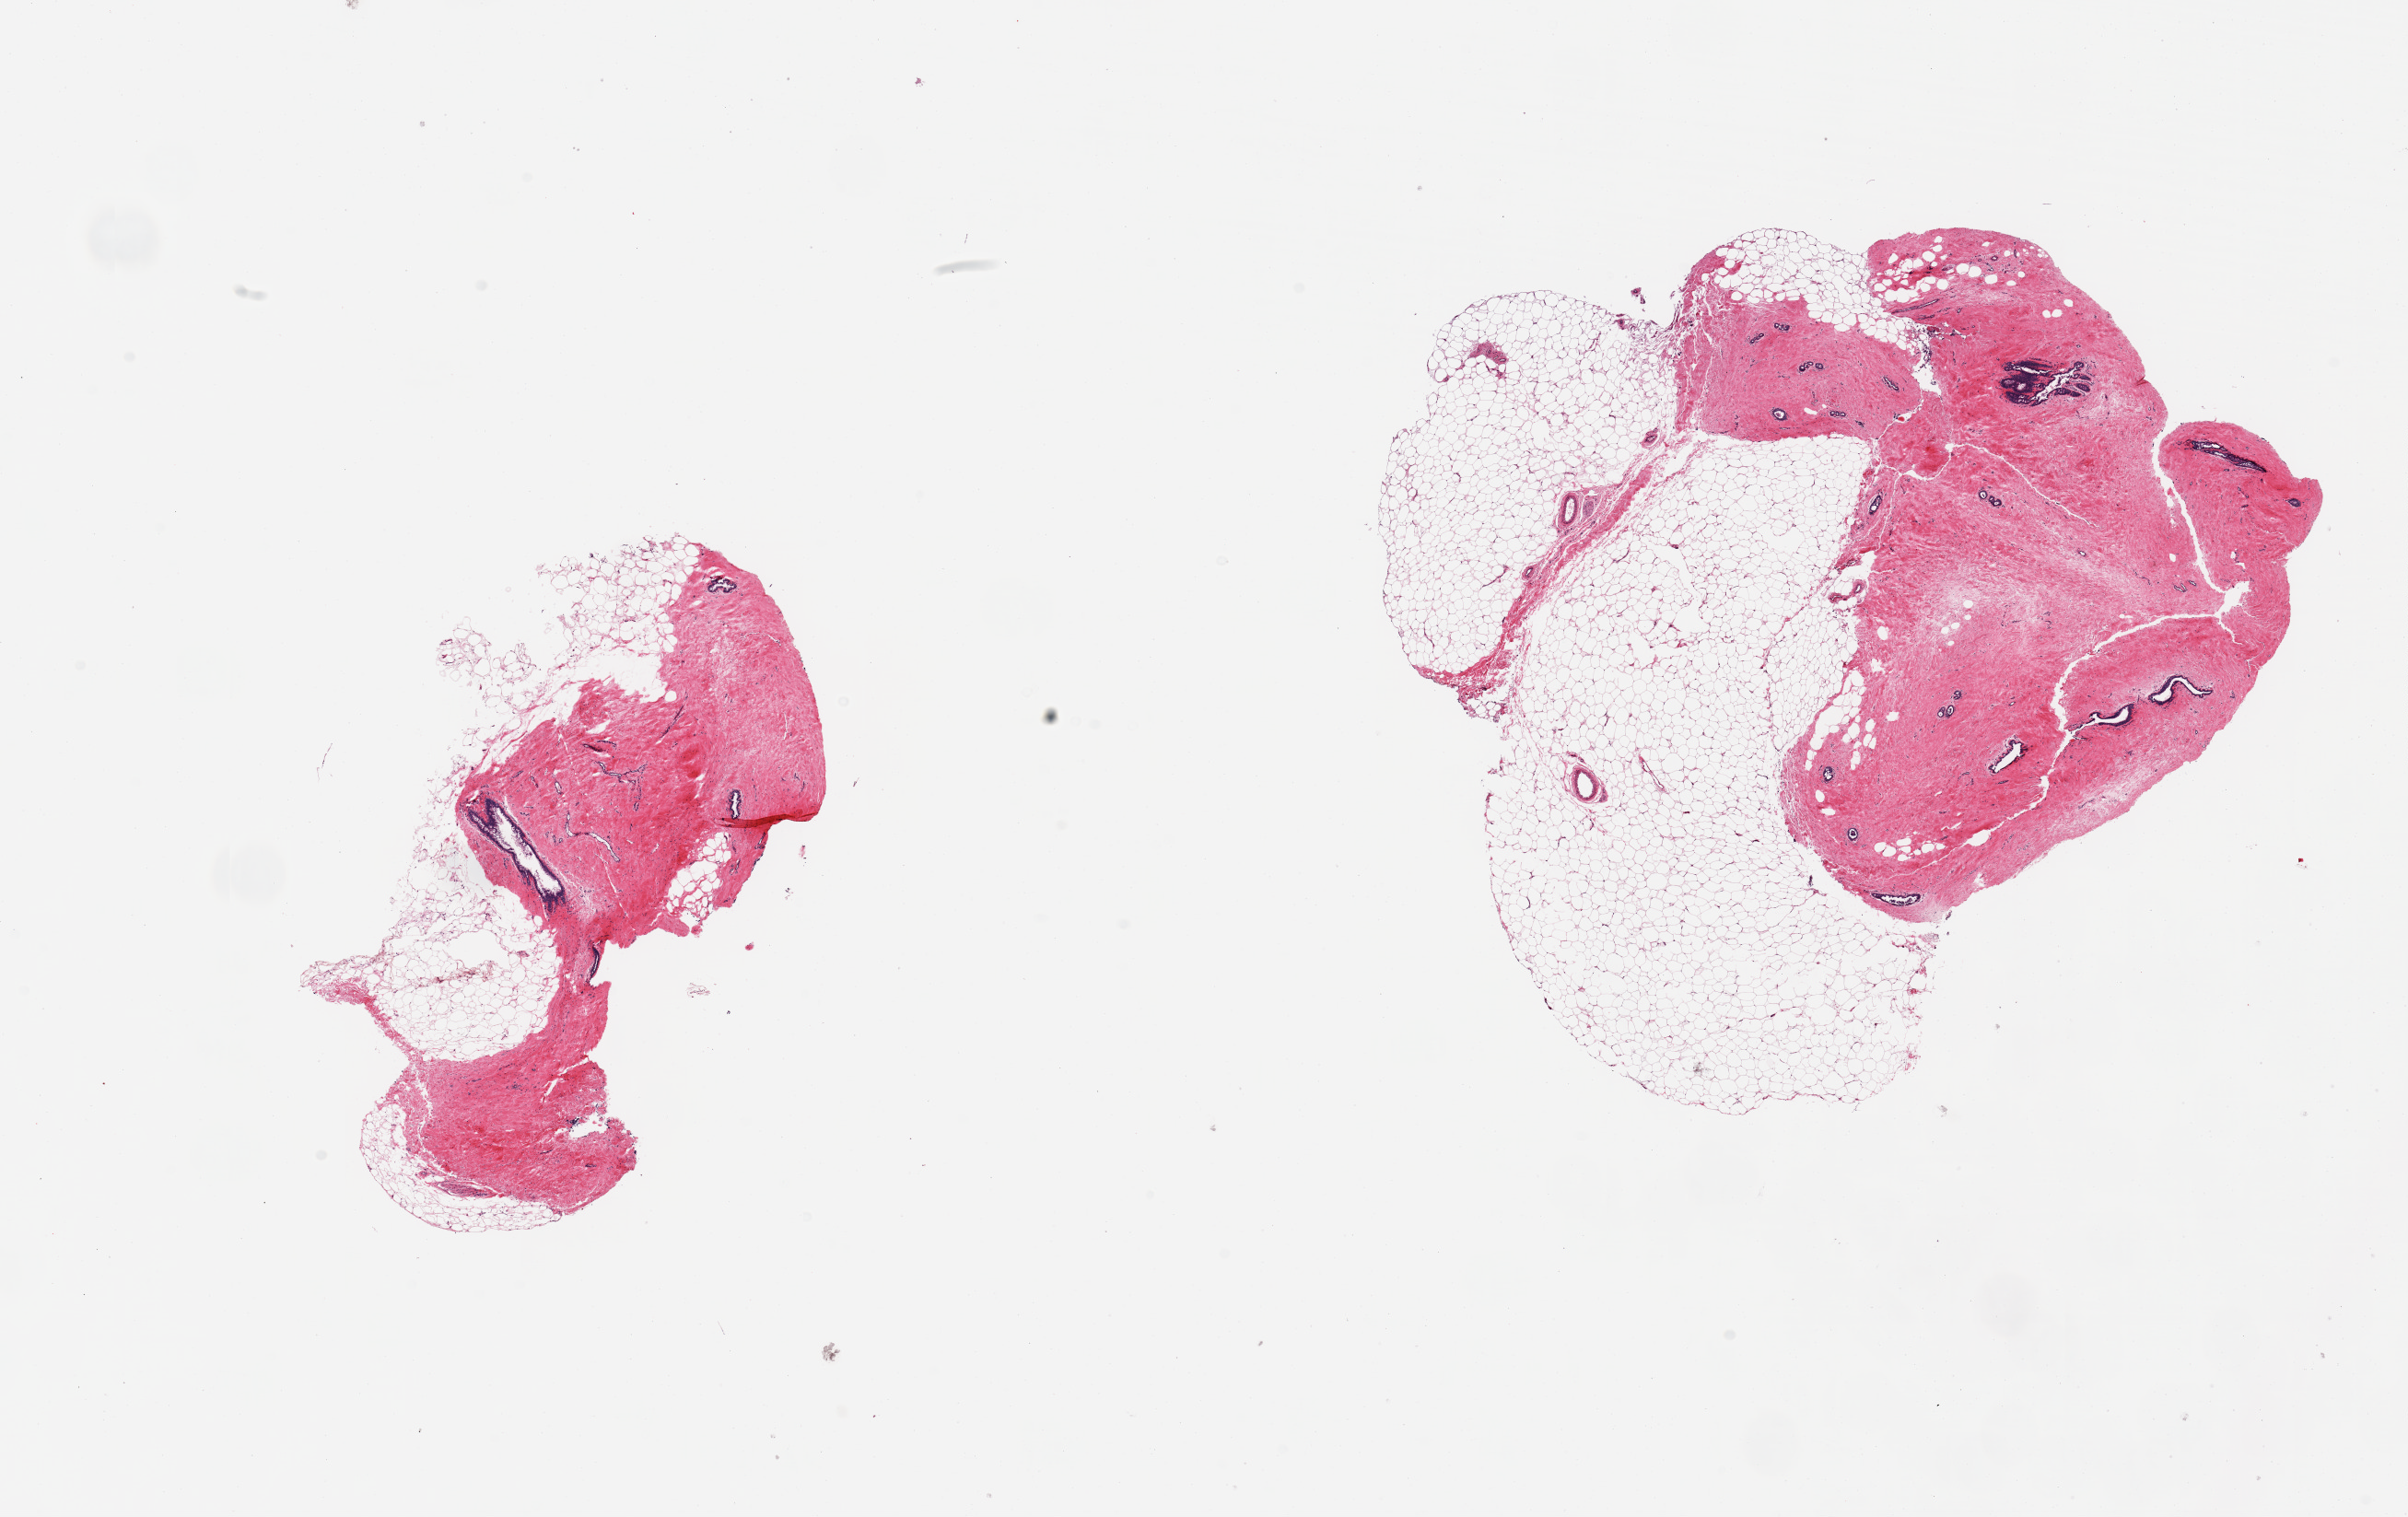
Digitized hematoxylin and eosin (H&E)-stained section — a low-resolution overview of the entire scanned area, about 20.7 x 13.0 mm (acquisition: 20x scan). PAXgene-fixed paraffin-embedded (PFPE) section. Sampled site (target tissue): breast. Donor tissue sample. Donor: male.
• pathologist's review note for this sample: 2 pieces, gynecomastoid stromal and ductal hyperplasia